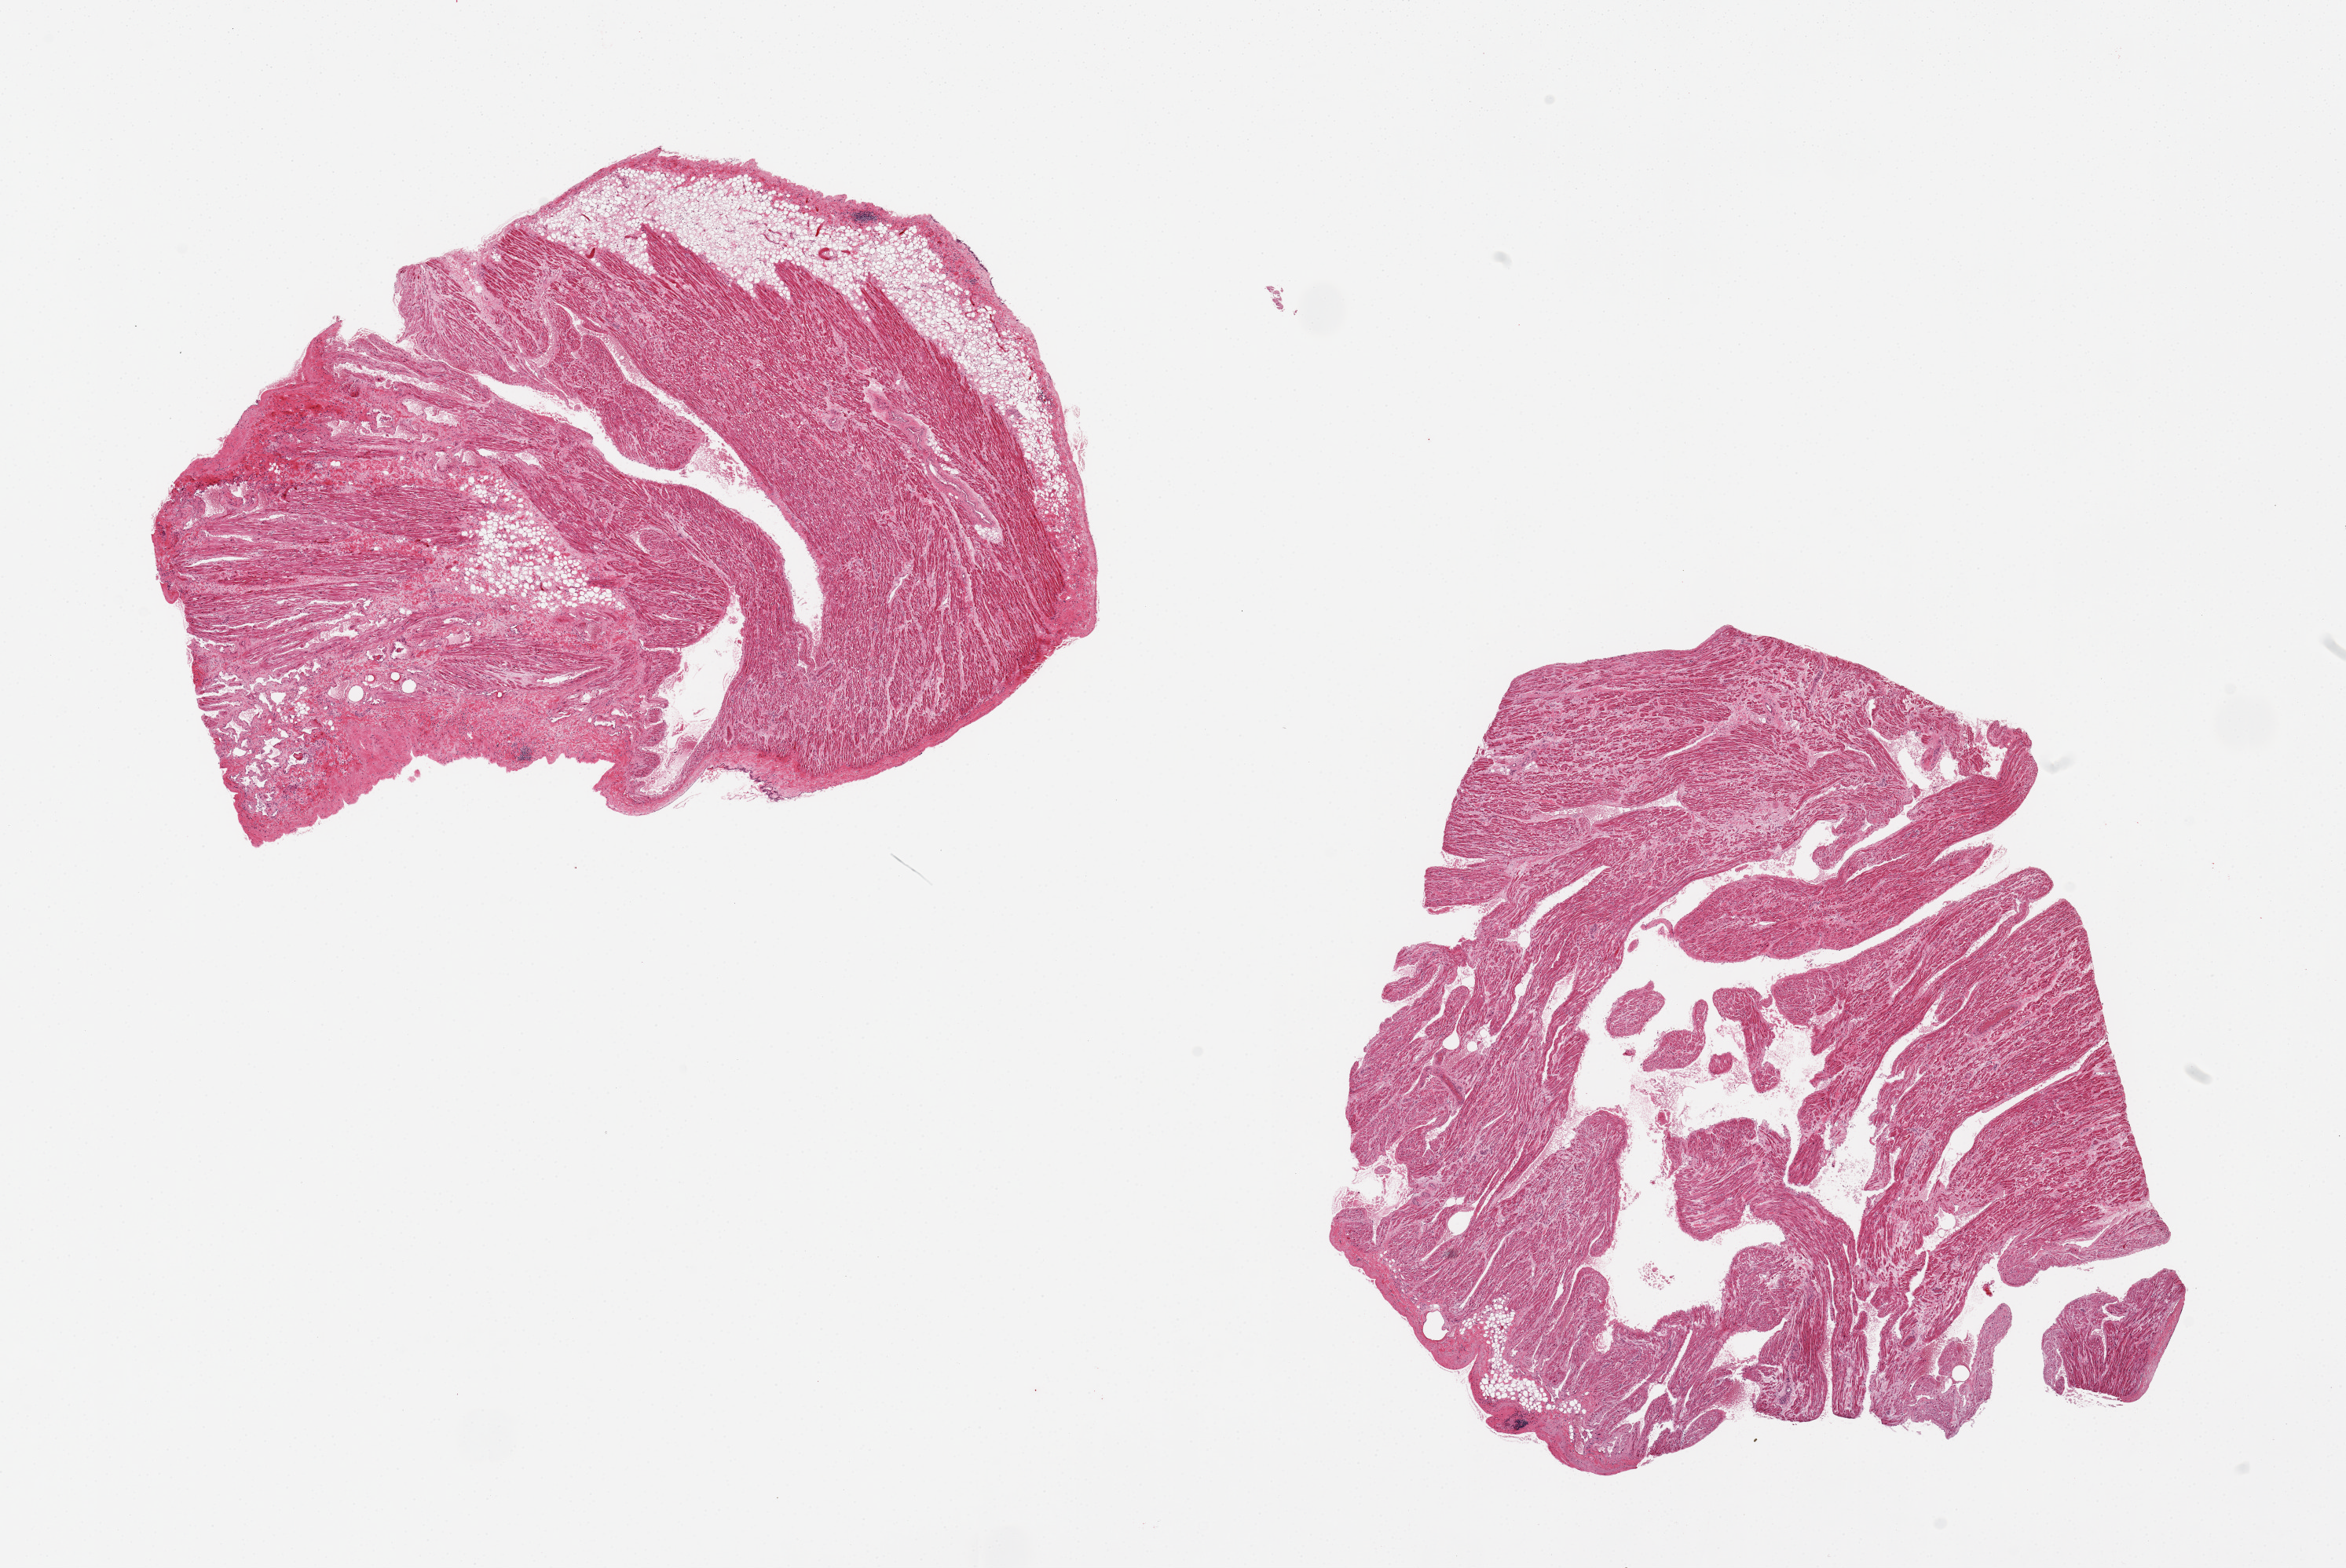
H&E whole-slide image, low-resolution overview of the scanned area, about 23.6 x 15.8 mm; PAXgene-fixed, paraffin-embedded tissue; sampled site (target tissue): auricular appendage; tissue donor sample. Donor: female.
Review note (as recorded): 2 pieces.